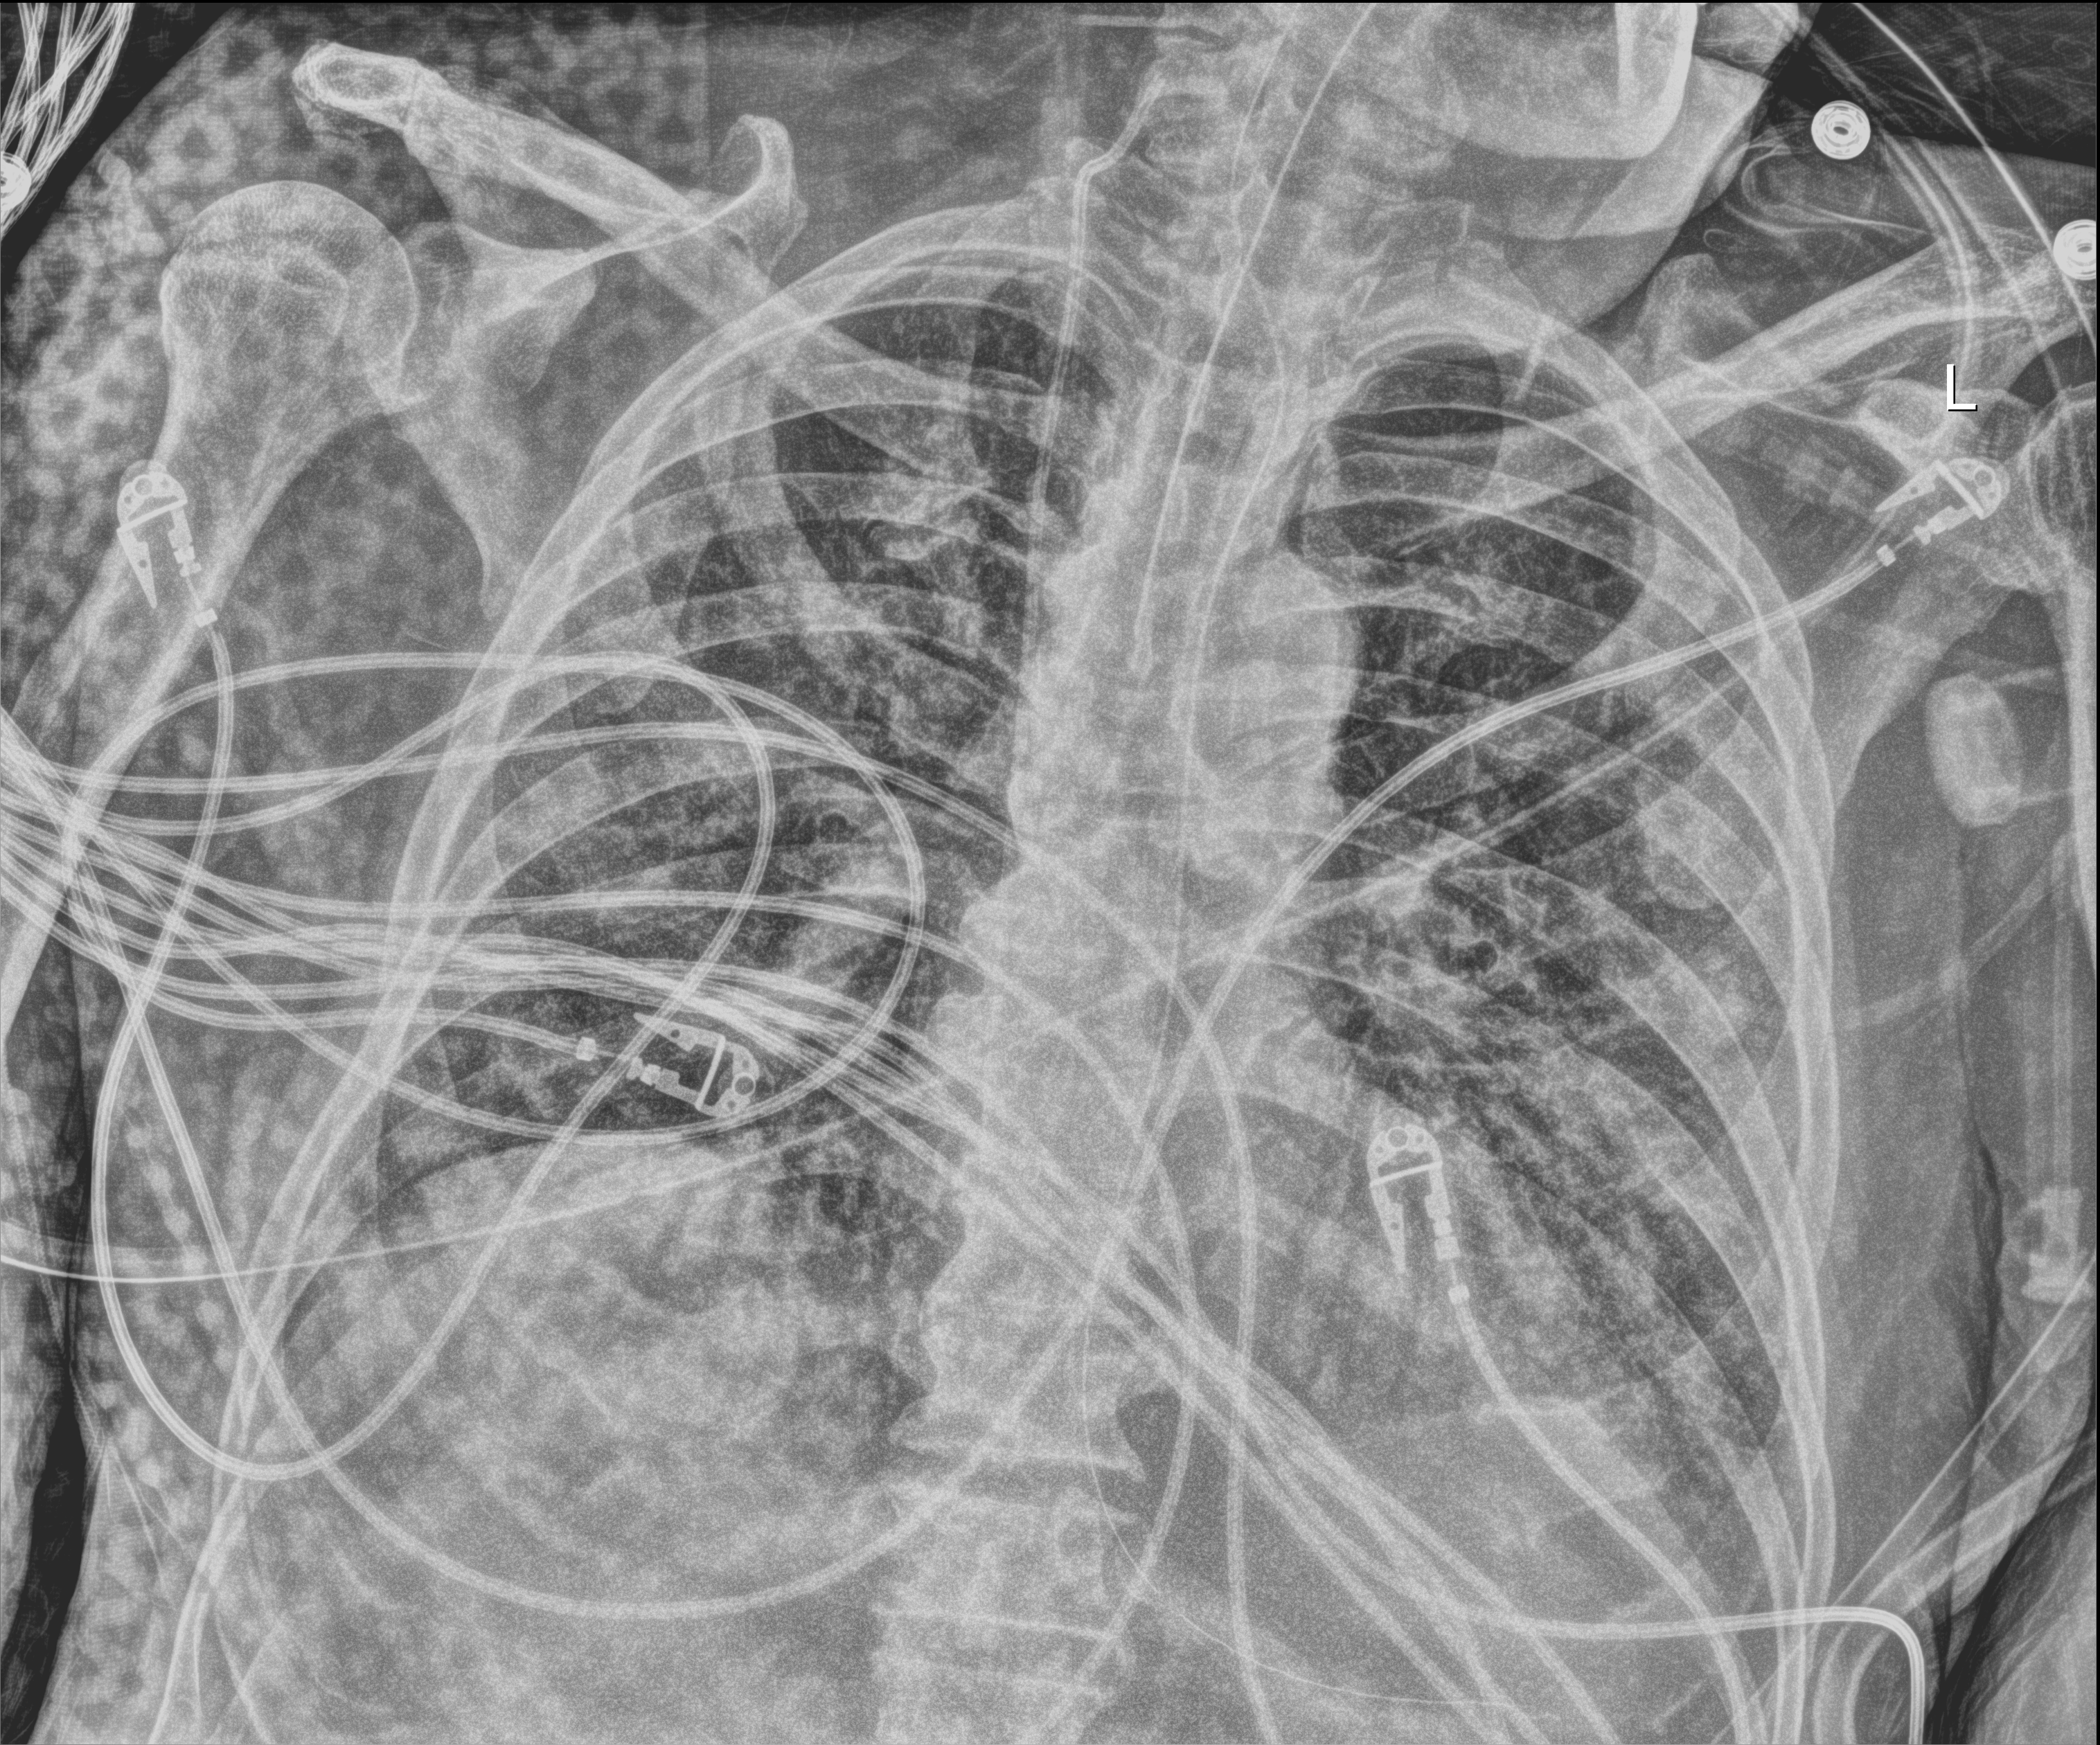
Chest X-ray (portable), anteroposterior (AP) projection. Male patient hospitalised with COVID-19, age 75–90 years.
From the hospital-stay record, not from the radiograph (when in the stay this image was taken is not recorded):
- mechanically ventilated during this hospital stay: yes
- smoking status (admission record): former